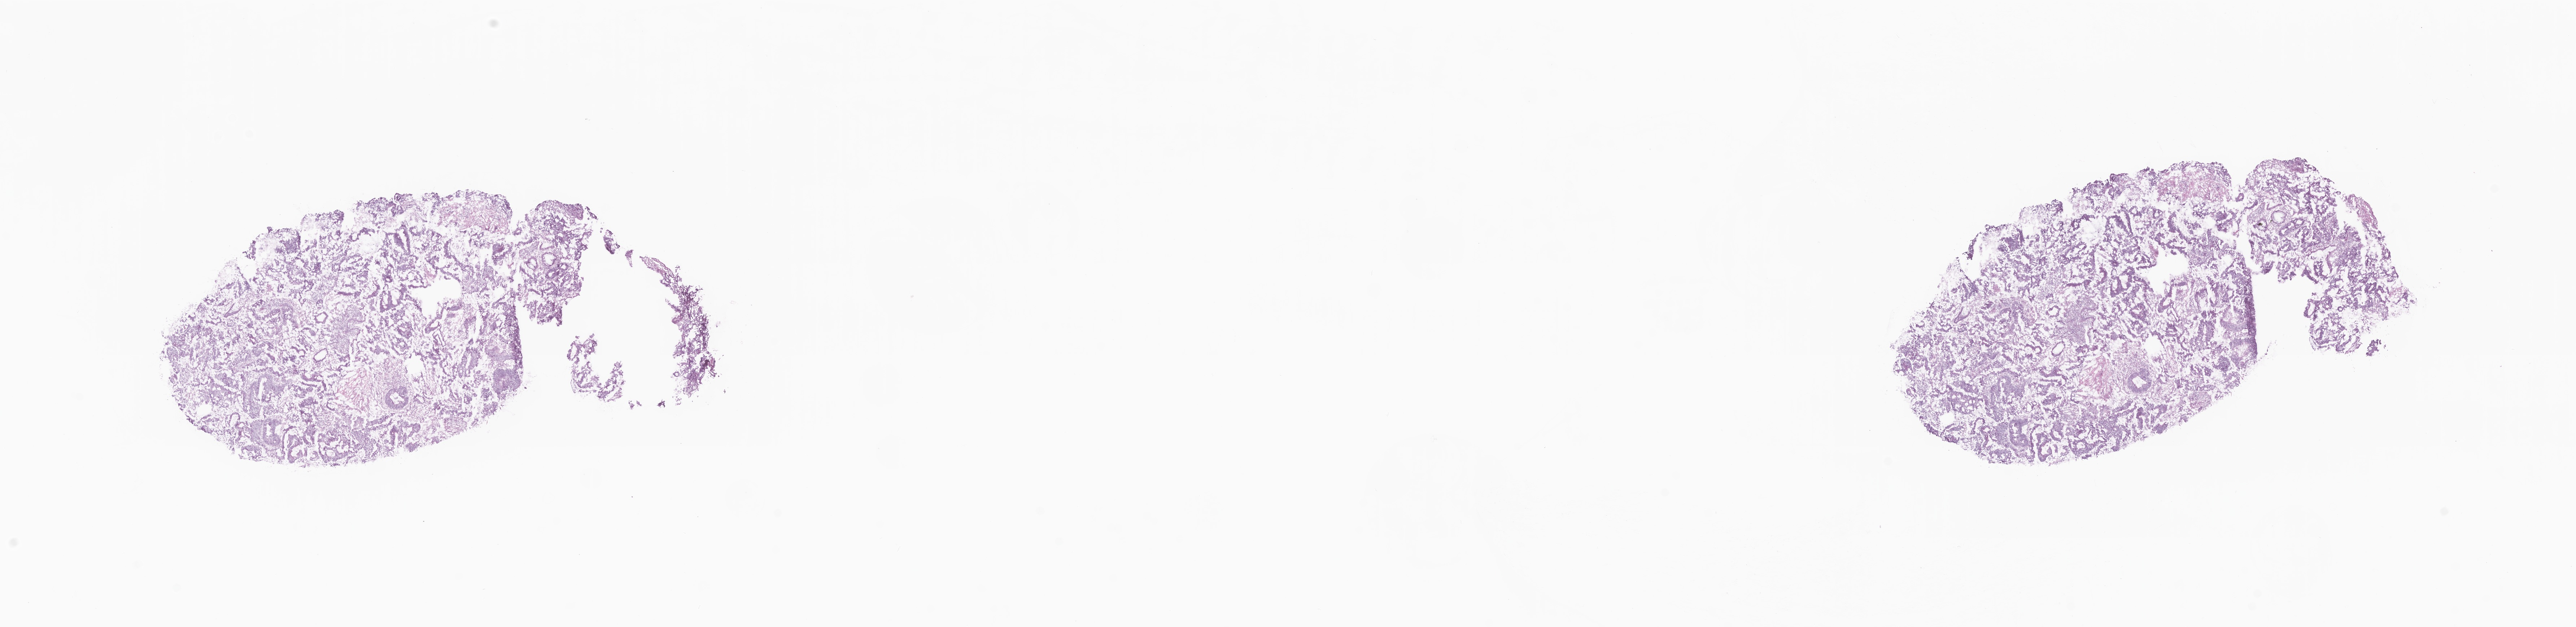
Whole-slide image, haematoxylin and eosin stain — shown as a low-resolution overview of the whole scanned area (about 30.1 x 7.3 mm); cryosection; specimen: primary tumor; anatomic site: sigmoid colon. Female, age 62 years at initial diagnosis. Tumor grade: G1 (well differentiated). Slide review estimates, as recorded: tumor cells 63%, tumor nuclei 70%, stromal cells 35%, necrosis 2%, normal cells 0%. Inflammatory infiltration, as recorded: lymphocyte infiltration 20%, monocyte infiltration 2%, neutrophil infiltration 0%.
- diagnosis: Adenocarcinoma, NOS
- section: top of the tissue portion
- AJCC pathologic stage: Stage IVB